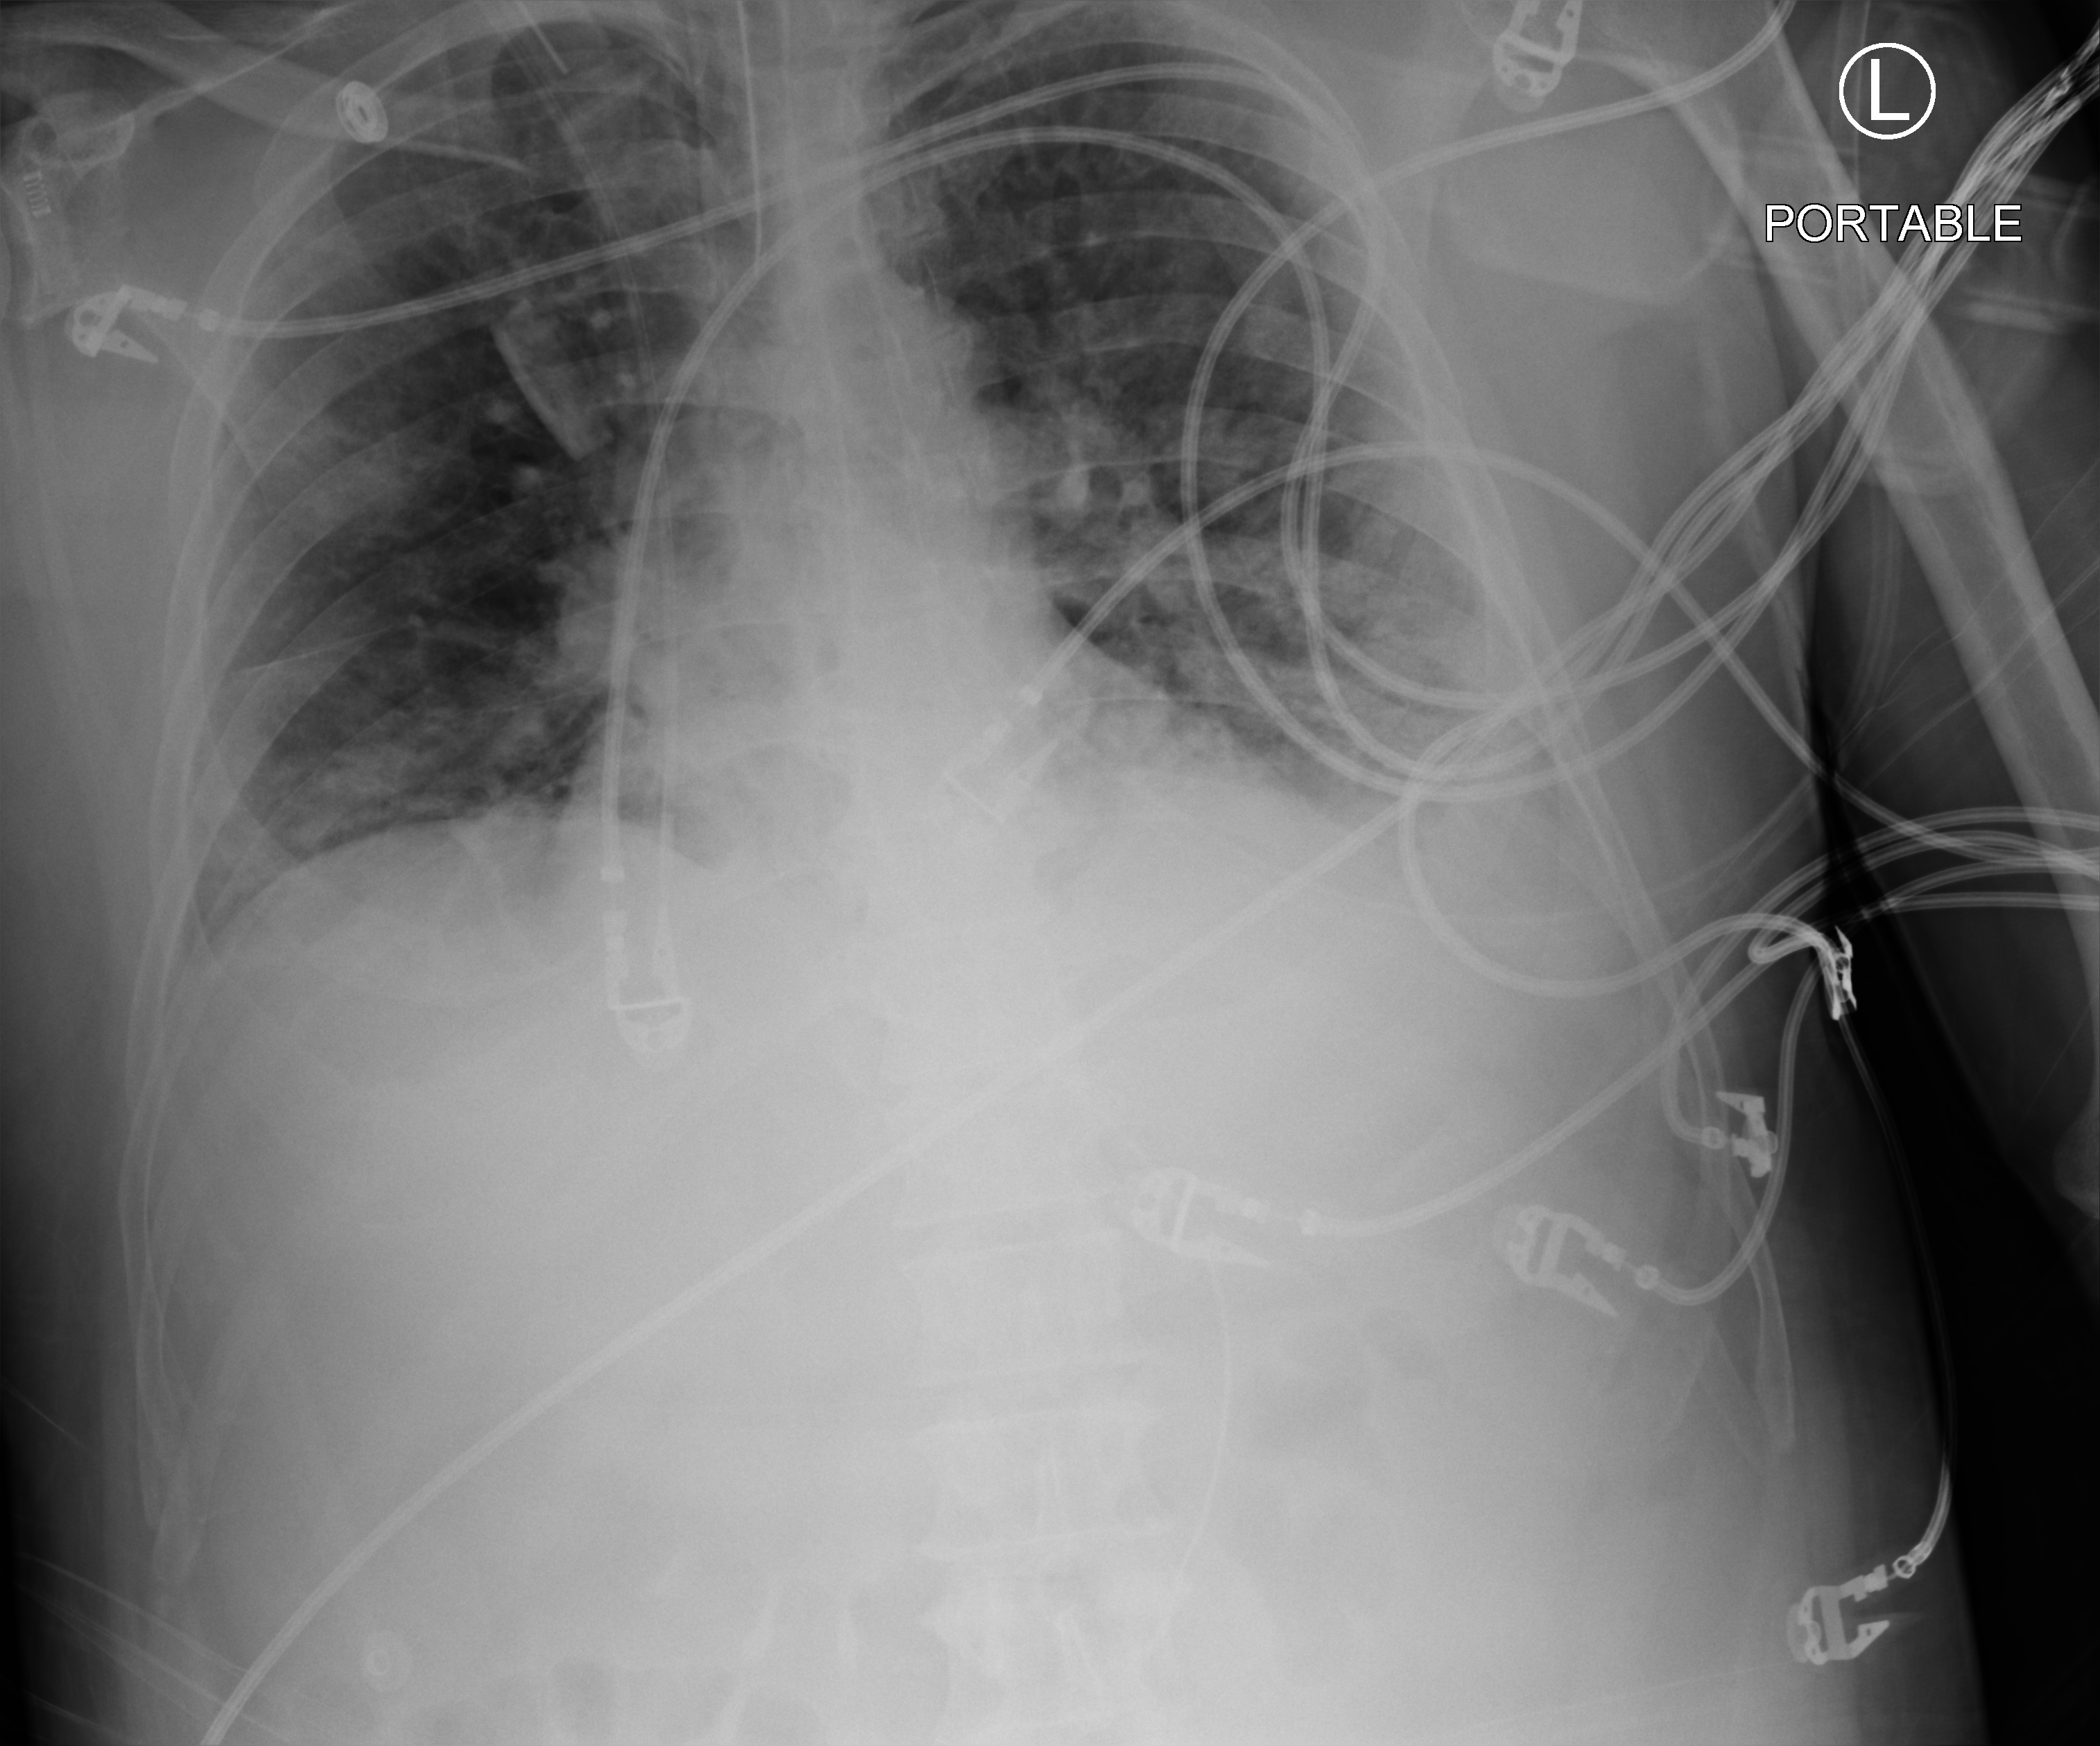
Portable chest radiograph; anteroposterior (AP) projection. Male patient hospitalised with COVID-19, age 18–59 years.
From the hospital-stay record, not from the radiograph (when in the stay this image was taken is not recorded):
- chronic kidney disease (admission record): no
- admitted to intensive care during this hospital stay: yes
- mechanically ventilated during this hospital stay: yes